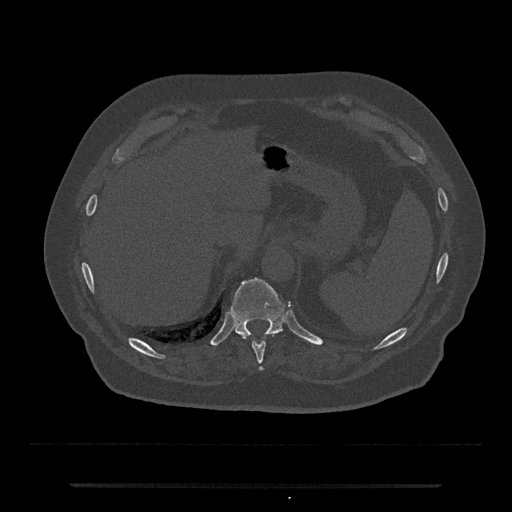
CT including the spine, one axial slice; slice 674 of 797 in the series (ordered by position); reconstruction kernel Br40s/3; 120 kVp; bone window (W 1800 / L 400 HU); 512 × 512 image matrix, field of view 434 × 434 mm. Patient: male, 80 years. Case-level facts recorded for this patient, not image findings: primary cancer: prostate; vertebrae with lytic lesions (as recorded): L1, T11.
Annotated regions visible in this slice (semi-automatic segmentation, software-assisted and operator-edited):
- T10 vertebra: bounding box <252,334,275,371> (left, top, right, bottom; pixels)
- T11 vertebra: <231,278,285,336>